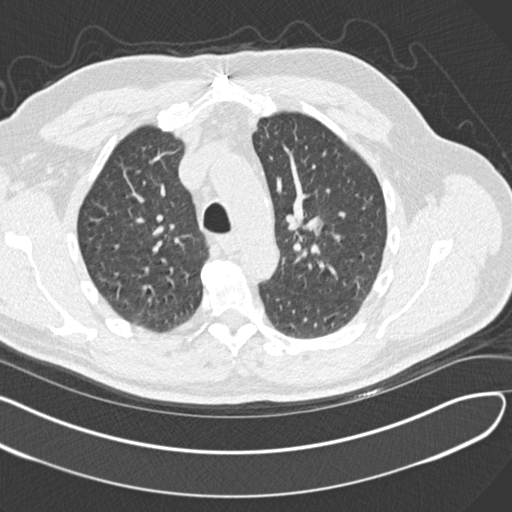
Chest CT (low-dose screening protocol), one axial image; second screening round (one year after baseline); lung window (W 1500 / L -600 HU); 2 mm slice thickness; slice 42 of 164 in the series. Male participant, aged 65 years at enrolment.
Lesion marked by an expert reader, bounding box (x1, y1, x2, y2) in pixels: (284, 197, 338, 257). The screening reader recorded 4 non-calcified nodules or masses ≥4 mm on this exam (left upper lobe, left upper lobe, left lower lobe, right middle lobe); which of them this box marks is not recorded. Official screen result: positive, other. Lung cancer was diagnosed 577 days after this screen (after the third annual screen): acinar cell carcinoma, left upper lobe, stage IA (AJCC 6th edition), 25 mm at pathology.